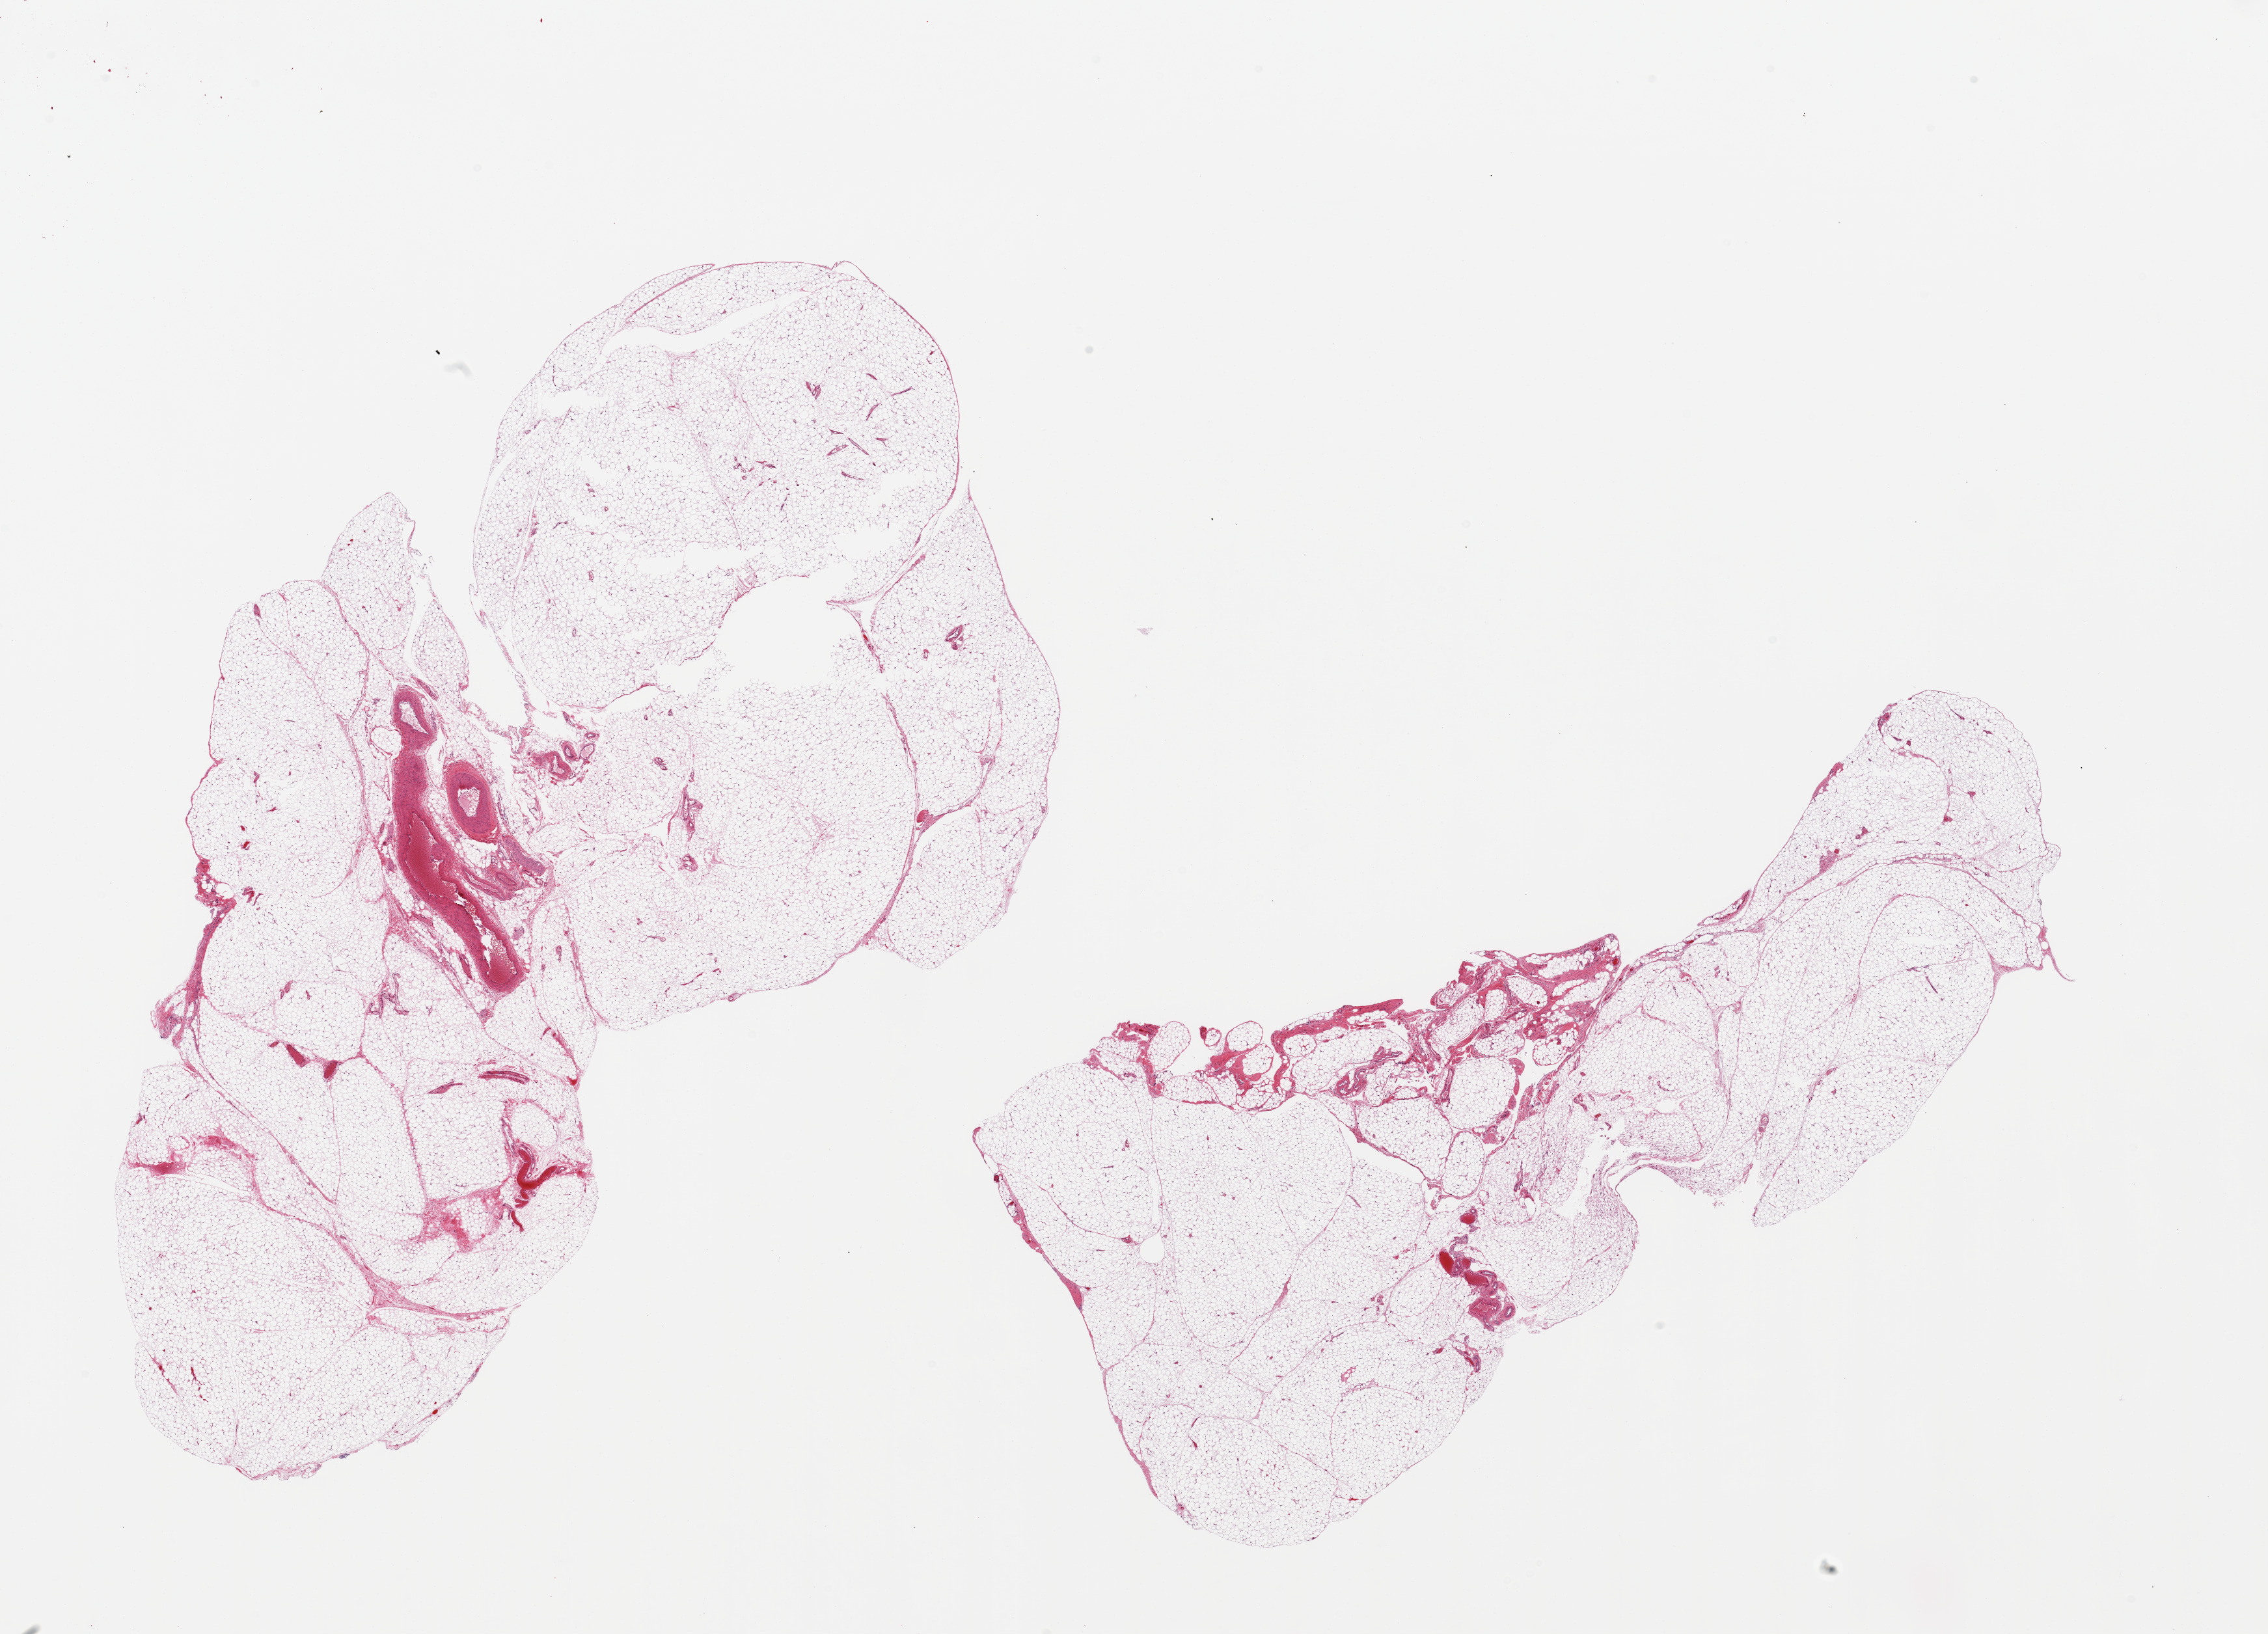
Digitized H&E-stained section — low-resolution overview of the scanned area, about 27.6 x 19.9 mm (from a 20x scan); PAXgene-fixed paraffin-embedded (PFPE) section; sampled site (target tissue): omentum; tissue donor sample.
Review note (as recorded): 2 pieces, ~10% fascia/vascular elements.